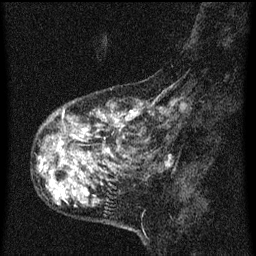
Breast MRI (dynamic contrast-enhanced), one sagittal slice. Slice 14 of 60 in the series (ordered by position). Dynamic contrast-enhanced series, image 2 of 3 at this slice position (ordered by acquisition). 1.5 T. TE 4.2 ms, TR 8 ms. 2 mm slice thickness. 256 × 256 image matrix. Female patient, age 55 years.
Outlined on this slice (semi-automatic segmentation, software-assisted and operator-edited):
- analysis volume of interest (the breast-tissue region the enhancement analysis was run in; not a lesion): bounding box <38,94,185,159> (left, top, right, bottom; pixels)
- tumour enhancement mask (voxels above the 70 % enhancement threshold inside the analysis volume of interest): <60,108,161,145>